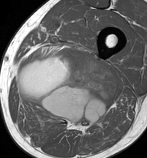
MRI of an extremity soft-tissue mass, one axial slice; slice 57 of 86 in the series (ordered by position); MR volume resampled by the dataset authors to the PET/CT grid (not the native acquisition matrix); 3.27 mm slice thickness; 147 × 158 image matrix. Male patient. Case-level facts recorded for this patient, not image findings: histological type: undifferentiated pleomorphic liposarcoma; grade: high; site of the primary tumour: left thigh.
Structures marked on this image (expert contour drawn on MRI and transferred to this co-registered scan by the dataset authors):
- gross tumour volume including surrounding oedema: box from (x=16, y=49) to (x=118, y=130) px
- gross tumour volume (mass): (x=16, y=49)–(x=118, y=127)